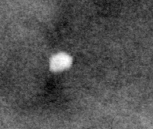
Region of interest cut from a scanned film mammogram (one marked finding); right breast; MLO view; BI-RADS breast density category 4 (scale 1–4).
Calcifications, morphology round and regular / lucent center / punctate, distribution diffusely scattered; BI-RADS assessment category 2; subtlety rating 5 on a 1 (subtle) to 5 (obvious) scale; benign without callback (not worked up further).